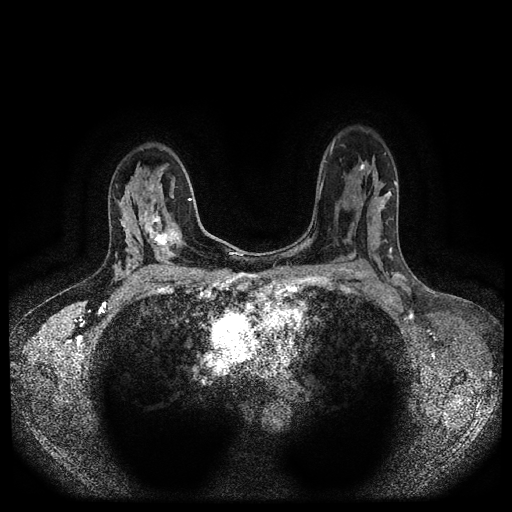
Breast MRI (dynamic contrast-enhanced, multi-phase), one axial slice. Position 67 of 116 along the scan axis. Dynamic contrast-enhanced series, time point 2 of 5 at this slice position (early post-contrast). 1.5 T. TE 2.6 ms, TR 5.4 ms. 2 mm slice thickness. 512 × 512 image matrix, field of view 340 × 340 mm. Patient: female, 47 years.
Outlined on this slice (semi-automatically segmented with operator editing):
- breast lesion (labelled 'tumour' in the annotation; benign lesions carry a separate 'benign' label): bounding box (x1, y1, x2, y2) in pixels: (135, 195, 181, 260)